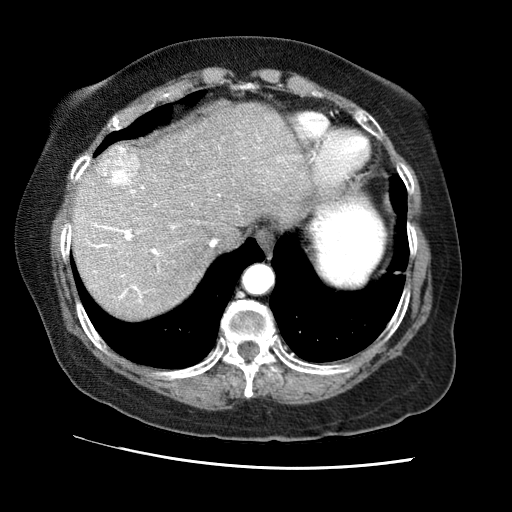
Contrast-enhanced abdominal CT (liver protocol), one axial slice; slice 55 of 65 in the series (ordered by position); reconstruction kernel STANDARD; soft-tissue window (W 400 / L 40 HU); 2.5 mm slice thickness; 512 × 512 image matrix. Case-level facts recorded for this patient, not image findings: diagnosis: hepatocellular carcinoma (patient treated with transarterial chemoembolisation; whether this scan precedes or follows treatment is not stated here); TNM stage (as recorded): Stage-II; Child-Pugh class: A; tumour differentiation: no biopsy; tumour size: 2.5 cm.
Structures marked on this image (semi-automatic segmentation, software-assisted and operator-edited):
- abdominal aorta: bounding box (x1, y1, x2, y2) in pixels: (244, 266, 273, 294)
- liver parenchyma outside the tumour (the mass and vessels are separate outlines, so this box may not span the whole liver): (72, 102, 315, 318)
- mass: (95, 146, 139, 185)
- liver vessels: (91, 160, 280, 302)